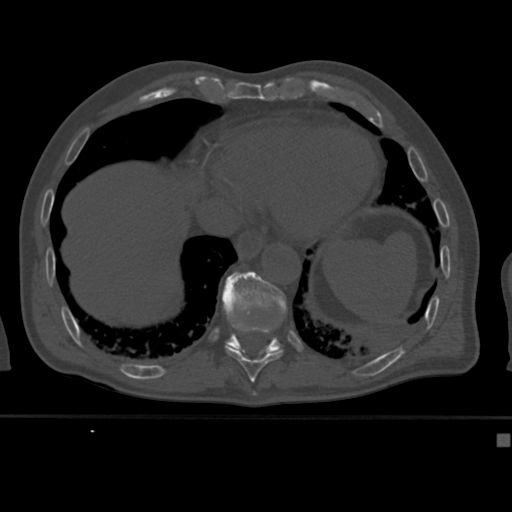
CT including the spine, one axial slice; slice 222 of 430 in the series (ordered by position); reconstruction kernel Br40s; 120 kVp; bone window (W 1800 / L 400 HU); 1.5 mm slice thickness; 512 × 512 image matrix, field of view 337 × 337 mm. Male patient, age 64 years. Case-level facts recorded for this patient, not image findings: primary cancer: uterus.
Structures marked on this image (semi-automatic segmentation, software-assisted and operator-edited):
- T10 vertebra: box from (x=225, y=326) to (x=283, y=382) px
- T11 vertebra: (x=222, y=271)–(x=287, y=355)